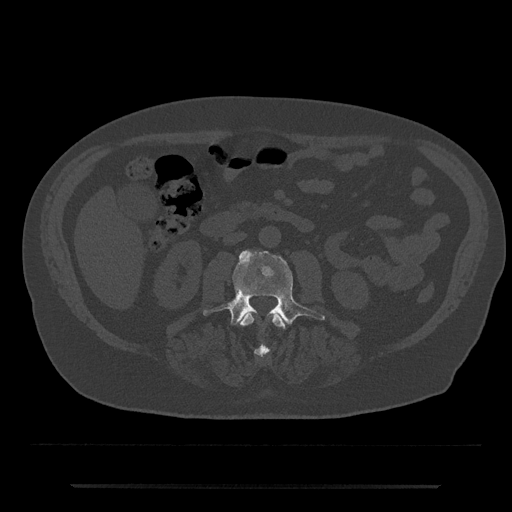
CT including the spine, one axial slice; slice 426 of 797 in the series (ordered by position); bone window (W 1800 / L 400 HU); 0.5 mm slice thickness; 512 × 512 image matrix, field of view 434 × 434 mm. Male patient, age 80 years. Case-level facts recorded for this patient, not image findings: primary cancer: prostate.
Annotated regions visible in this slice (semi-automatic segmentation, software-assisted and operator-edited):
- L2 vertebra: bounding box (x1, y1, x2, y2) in pixels: (240, 311, 285, 357)
- L3 vertebra: (203, 250, 325, 325)